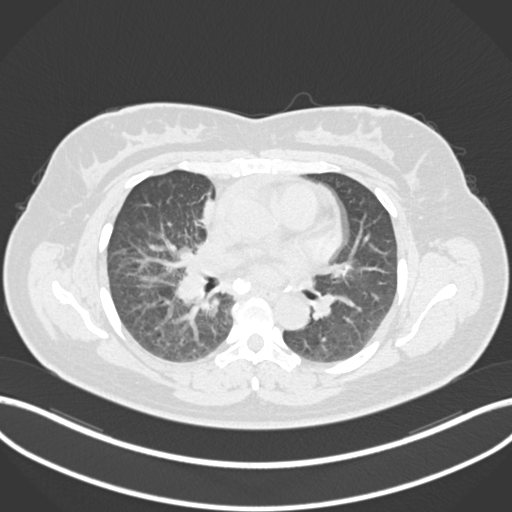
Chest CT, one axial slice; slice 88 of 183 in the series (ordered by position); 120 kVp; lung window (W 1500 / L -600 HU); 1 mm slice thickness; 512 × 512 image matrix, field of view 400 × 400 mm. Patient: female, 46 years. From the clinical record (not read from this slice): clinical TNM (as recorded): T2a N1 M0.
Annotated regions visible in this slice (bounding box drawn by a radiologist):
- lung tumour (recorded histology: adenocarcinoma): bounding box (x1, y1, x2, y2) in pixels: (196, 193, 222, 228)